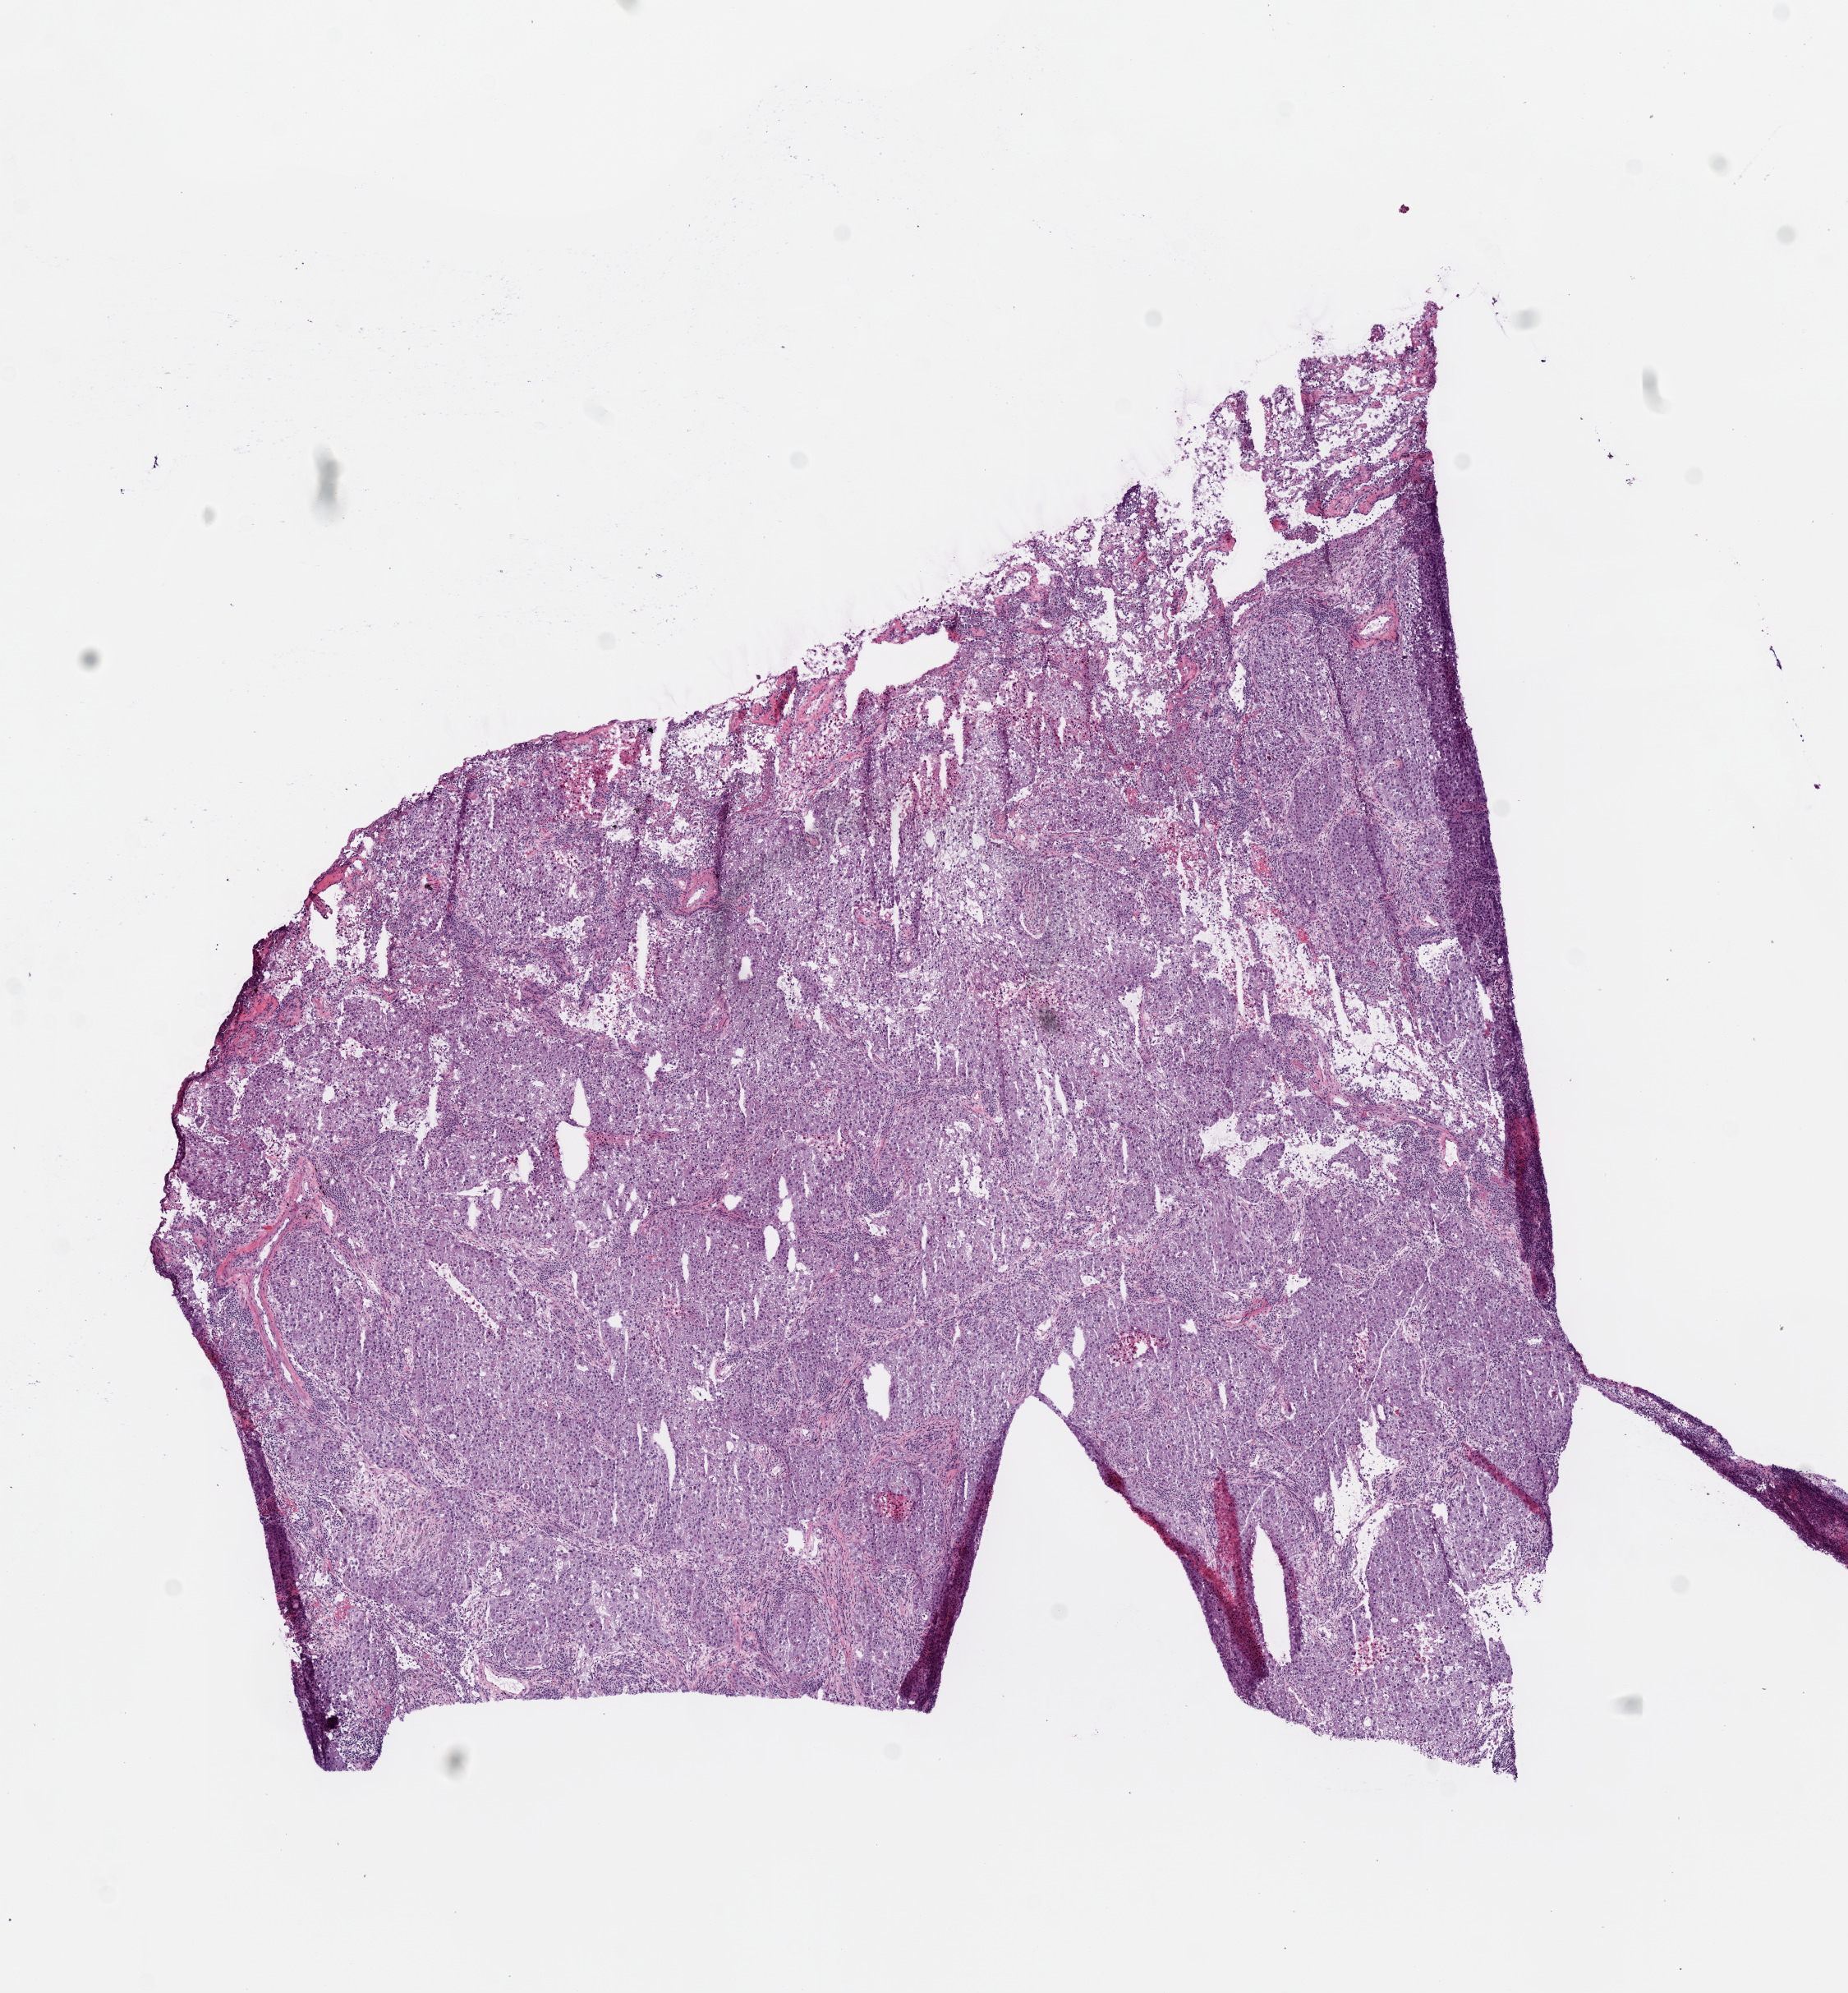
Whole-slide histology image, Hematoxylin and eosin (H&E) stained, low-resolution overview of the scanned area, about 9.0 x 9.7 mm. Frozen section. Sample: primary tumour, lung. Female patient; age at initial diagnosis 66 years. Composition of this section per pathologist review: tumour cells 89%, tumour nuclei 85%, normal cells 3%, stromal cells 5%, necrosis 3%.
* AJCC pathologic stage: IIB (6th edition)
* histologic diagnosis: Squamous cell carcinoma, NOS